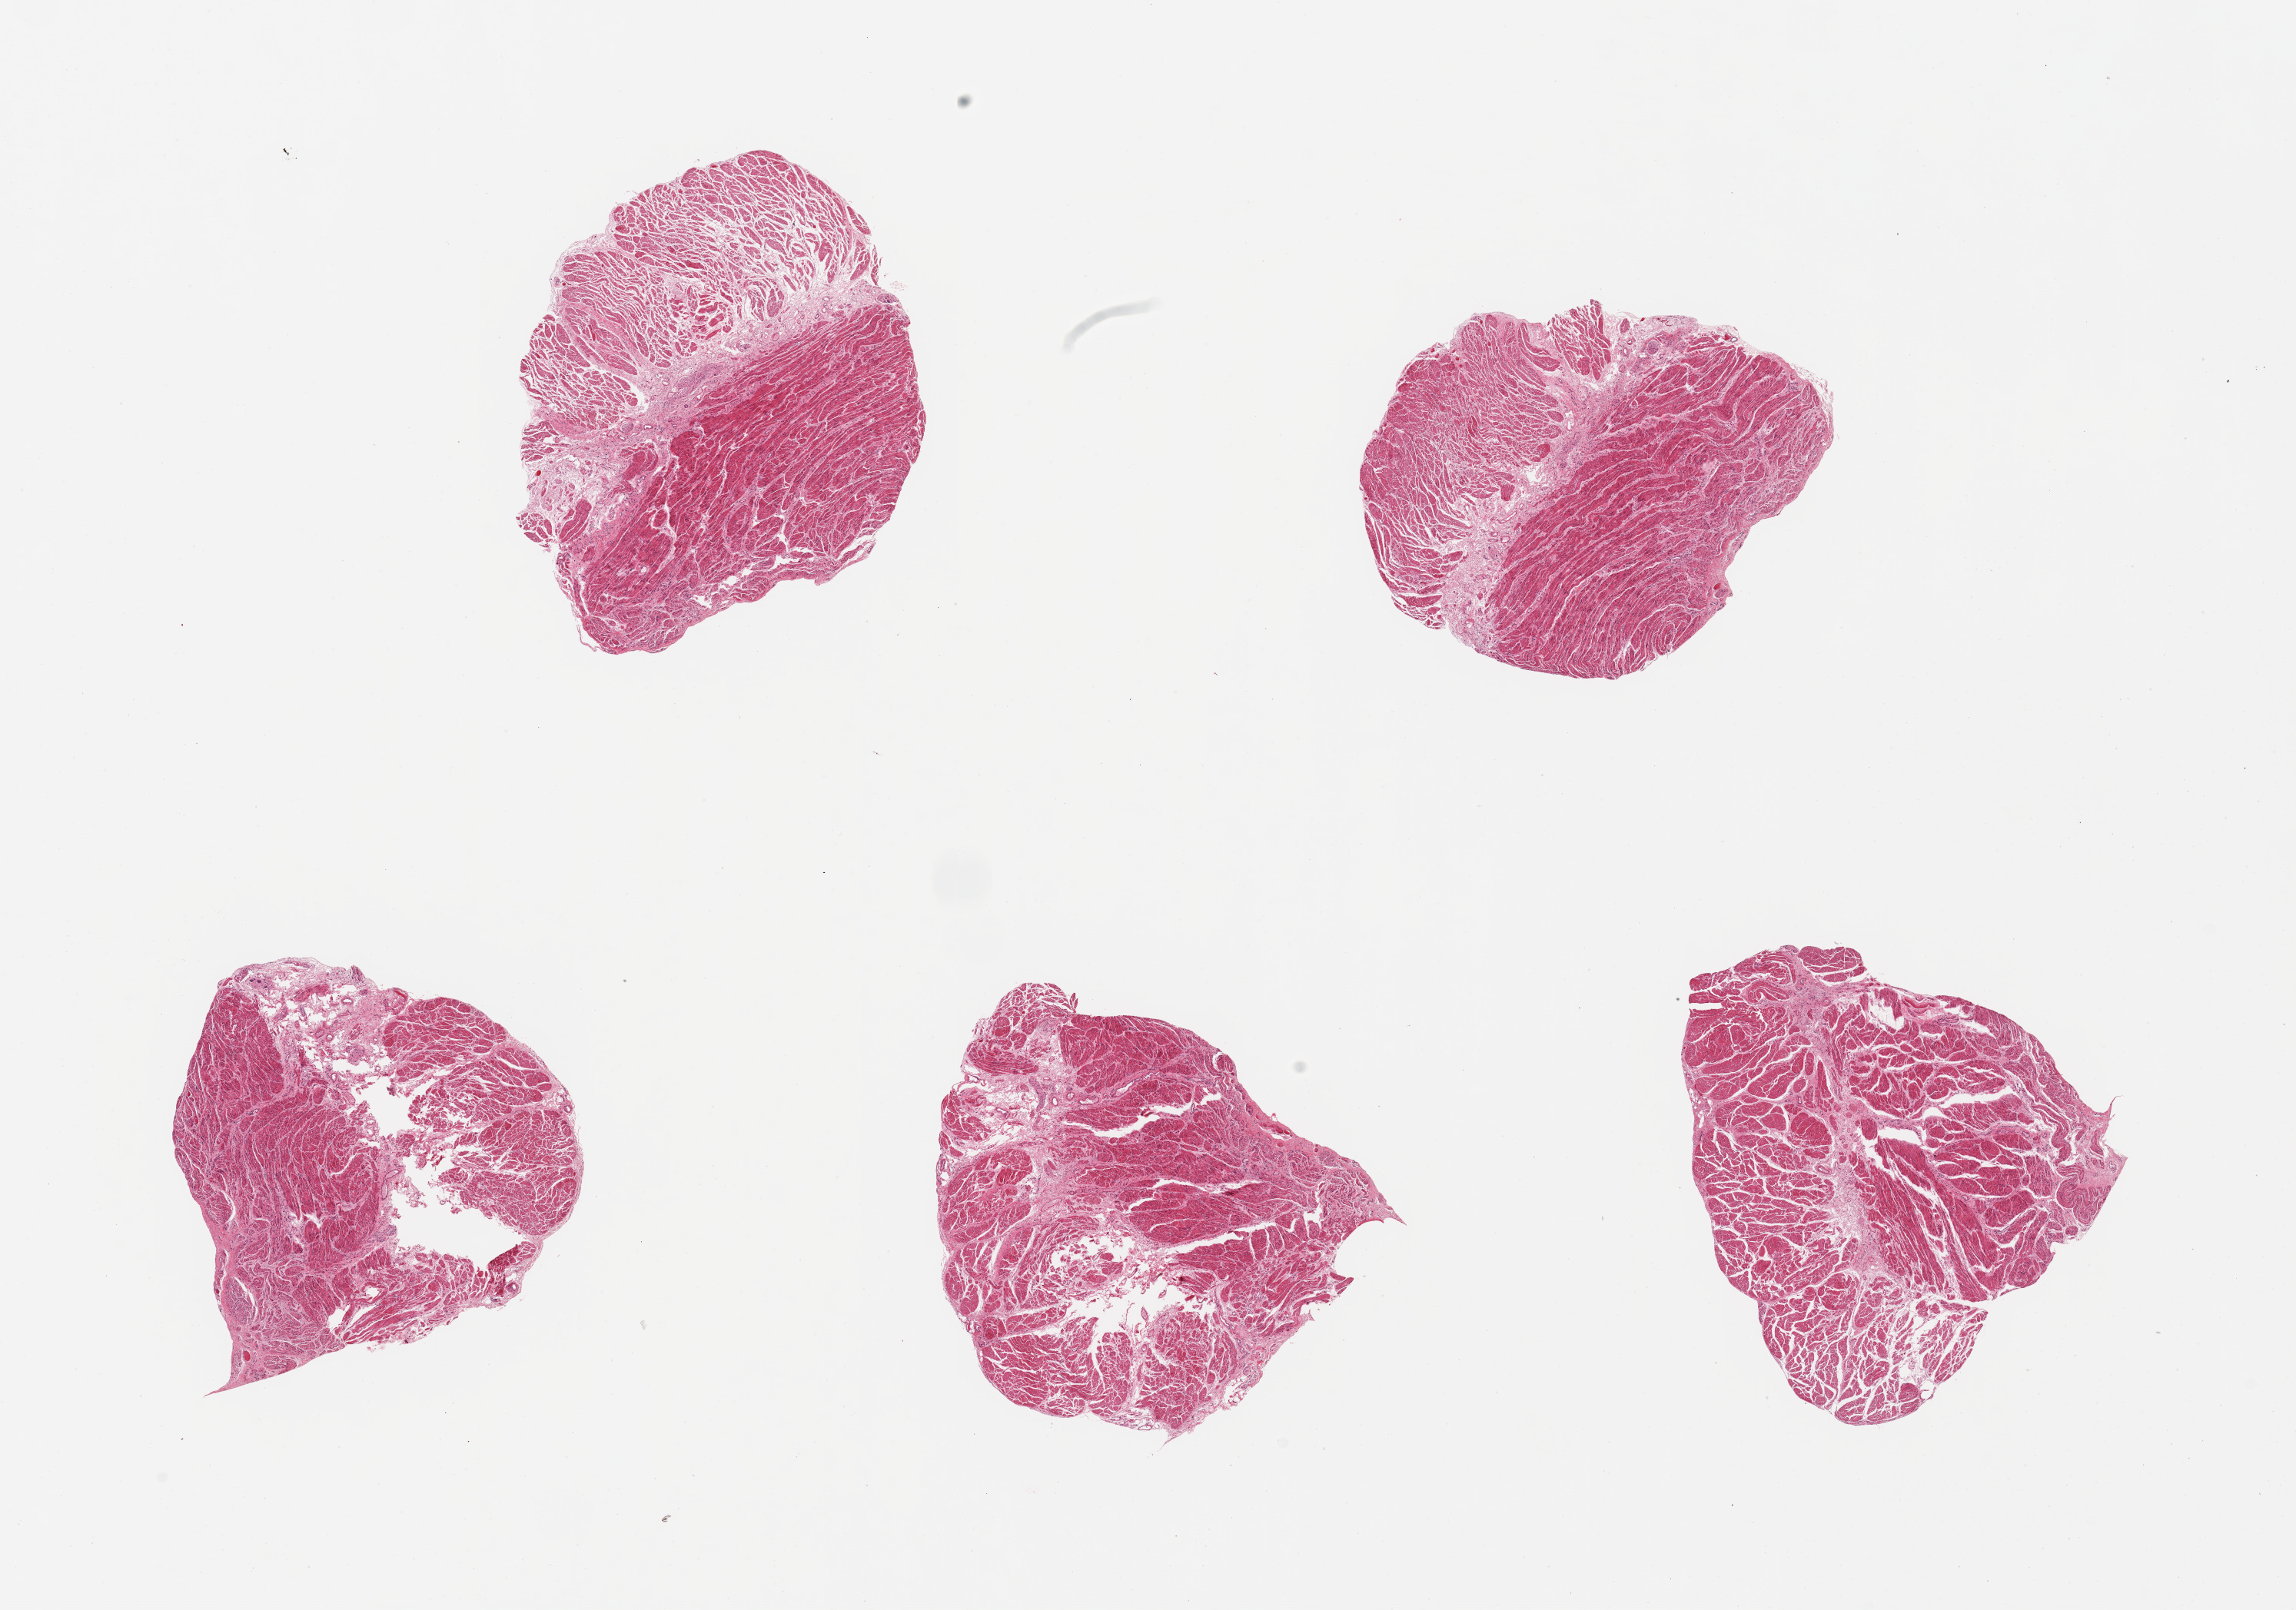
Hematoxylin and eosin (H&E) whole-slide image — shown as a low-resolution overview of the whole scanned area (about 23.6 x 16.6 mm). PAXgene-fixed paraffin-embedded (PFPE) section. Section of gastroesophageal junction (target tissue). Tissue donor sample. Donor: male.
Pathologist's review note for this sample: 5 pieces; well trimmed.